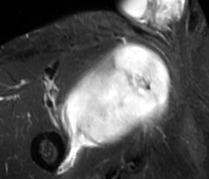
MRI of an extremity soft-tissue mass, one axial slice. Position 59 of 89 along the scan axis. STIR. MR volume resampled by the dataset authors to the PET/CT grid (not the native acquisition matrix). 3.27 mm slice thickness. 209 × 179 image matrix, field of view 204 × 175 mm. Male patient. Case-level facts recorded for this patient, not image findings: histological type: undifferentiated - pleiomorphic; grade: high; site of the primary tumour: right thigh.
Structures marked on this image (expert contour drawn on MRI and transferred to this co-registered scan by the dataset authors):
- gross tumour volume including surrounding oedema: box from (x=60, y=43) to (x=170, y=149) px
- gross tumour volume (mass): (x=60, y=43)–(x=170, y=149)